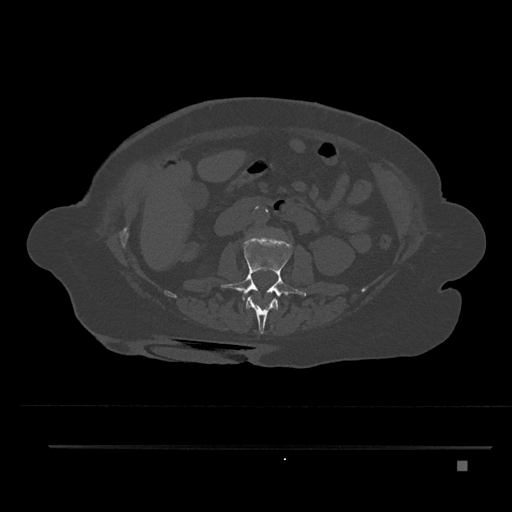
CT including the spine, one axial slice. Slice 178 of 797 in the series (ordered by position). Reconstruction kernel Br40s/3. 120 kVp. Bone window (W 1800 / L 400 HU). 0.5 mm slice thickness. 512 × 512 image matrix. Patient: female, 76 years. Case-level facts recorded for this patient, not image findings: primary cancer: lung.
Annotated regions visible in this slice (semi-automatic segmentation, software-assisted and operator-edited):
- L1 vertebra: bounding box (x1, y1, x2, y2) in pixels: (246, 296, 279, 334)
- L2 vertebra: (221, 237, 307, 301)